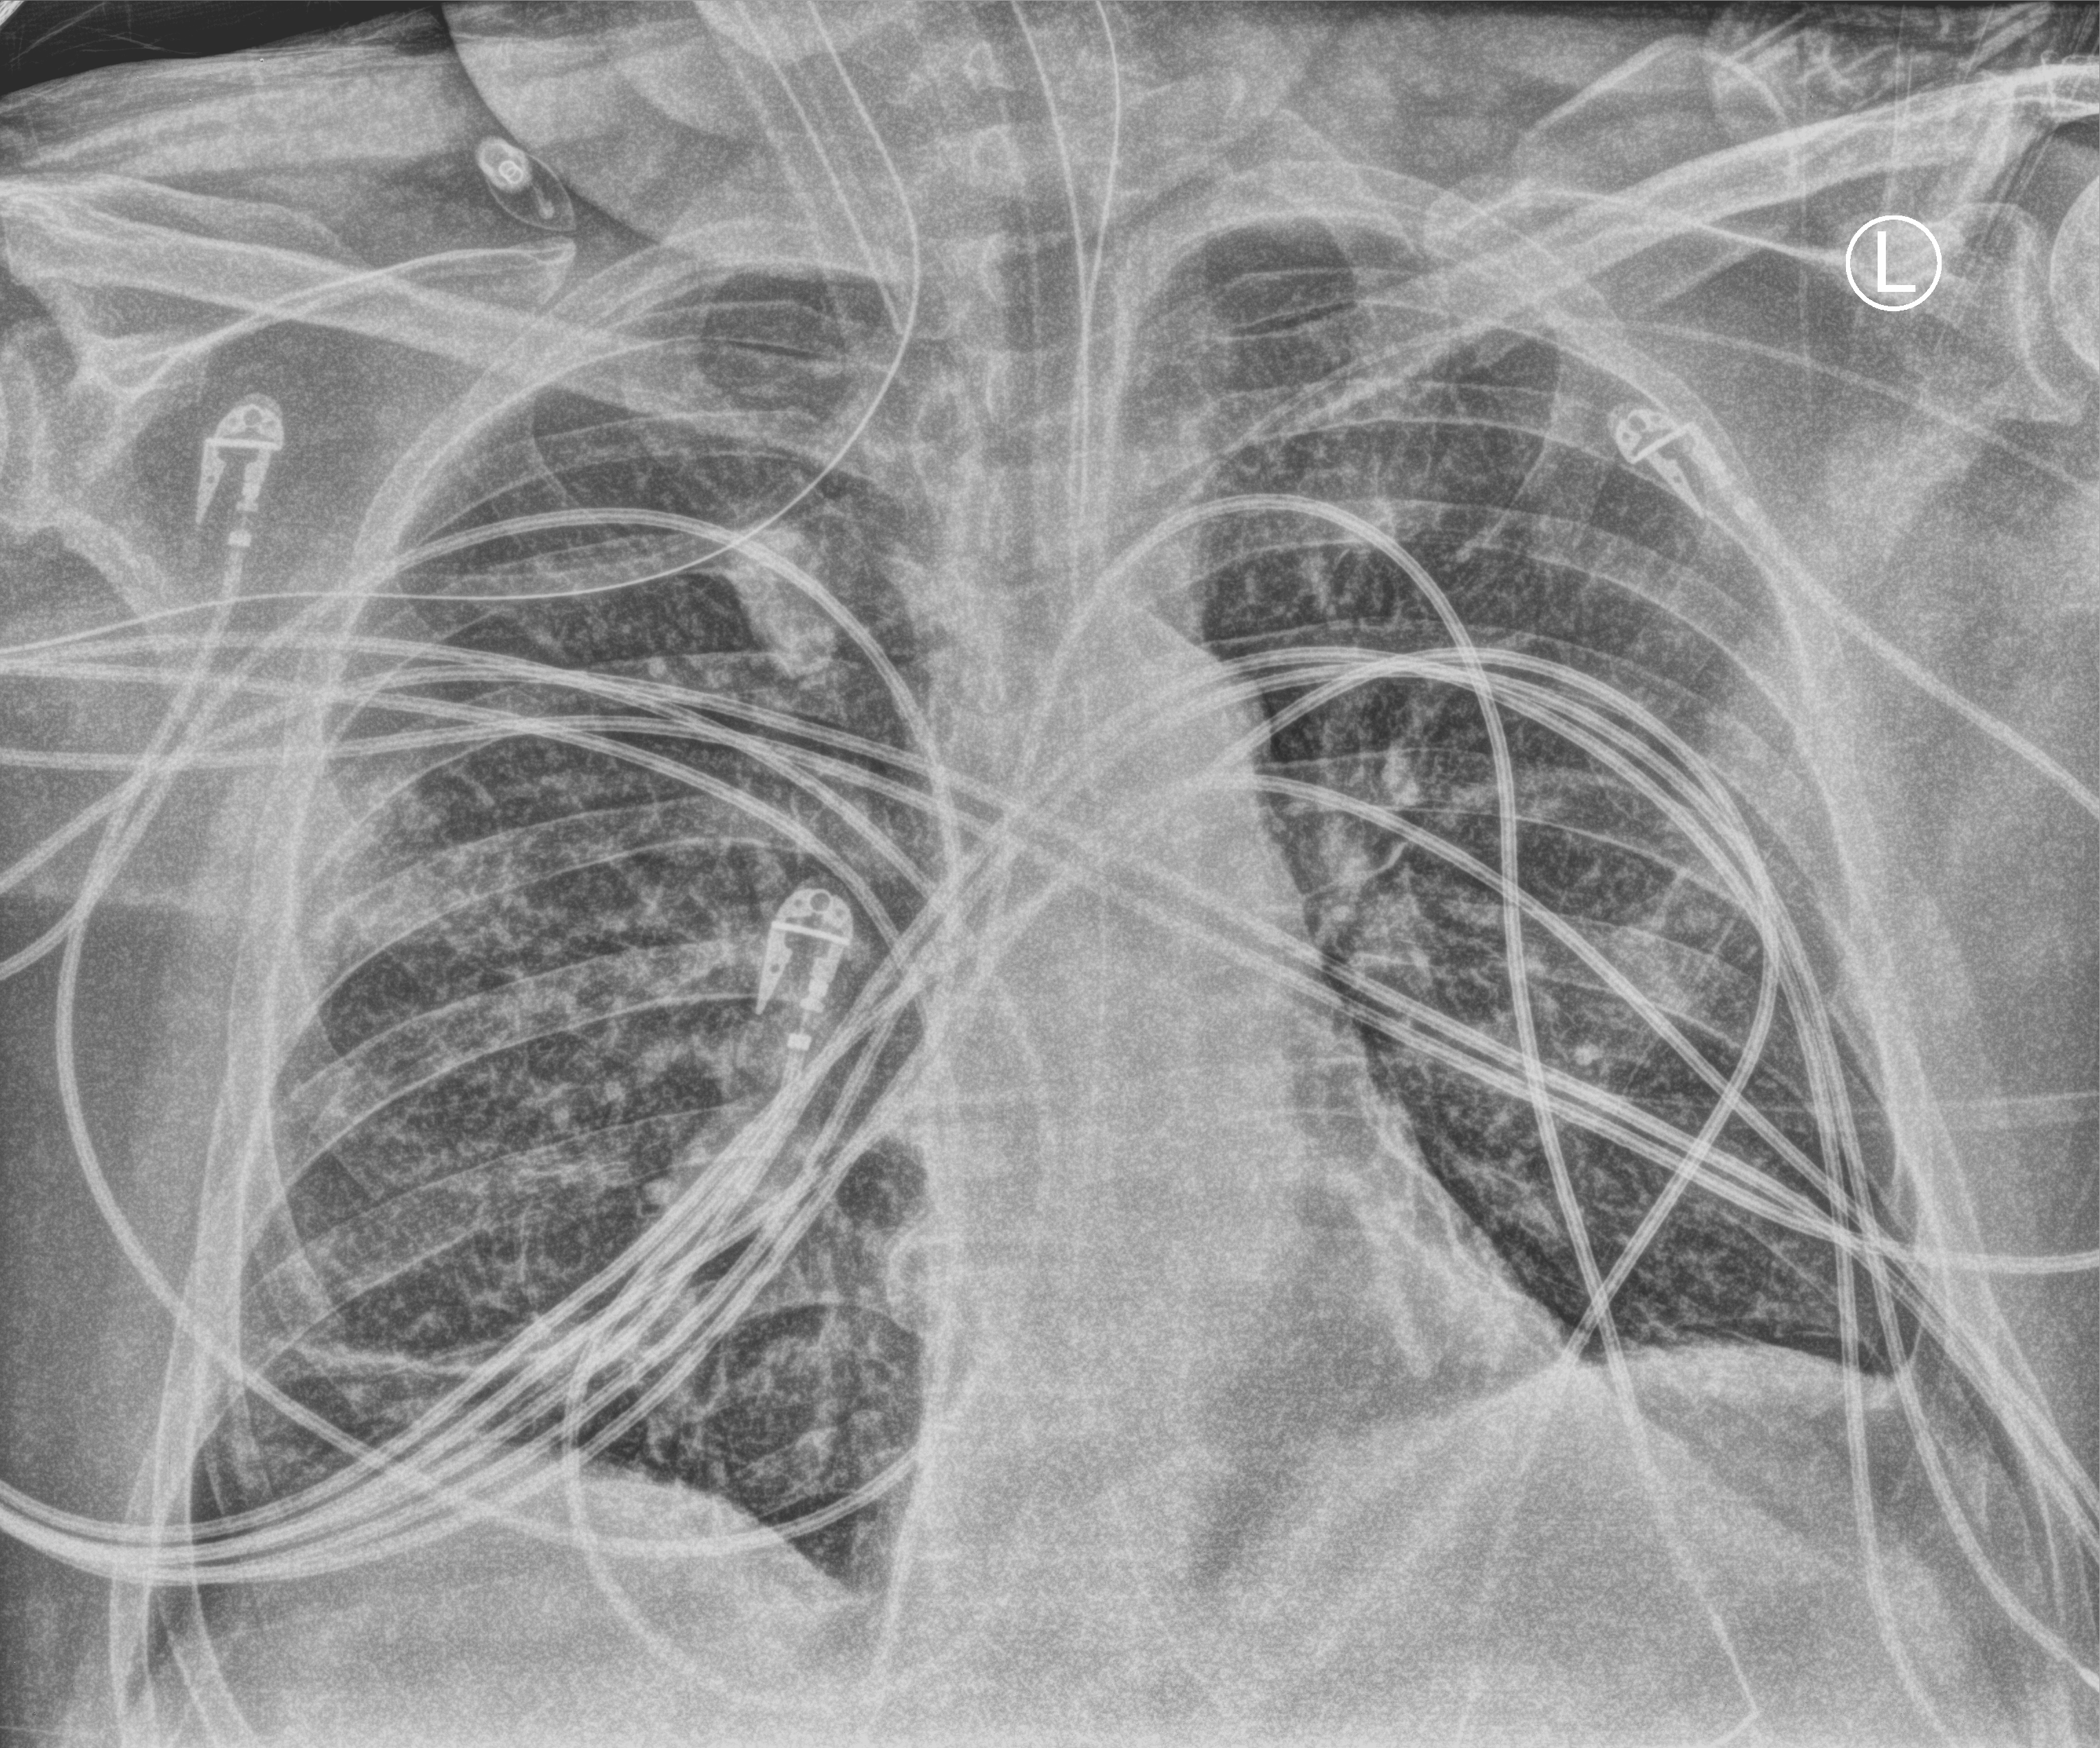
Chest X-ray (portable). Male patient hospitalised with COVID-19, age 60–74 years.
From the hospital-stay record, not from the radiograph (when in the stay this image was taken is not recorded):
- admitted to intensive care during this hospital stay: yes
- smoking status (admission record): never
- COPD (admission record): no